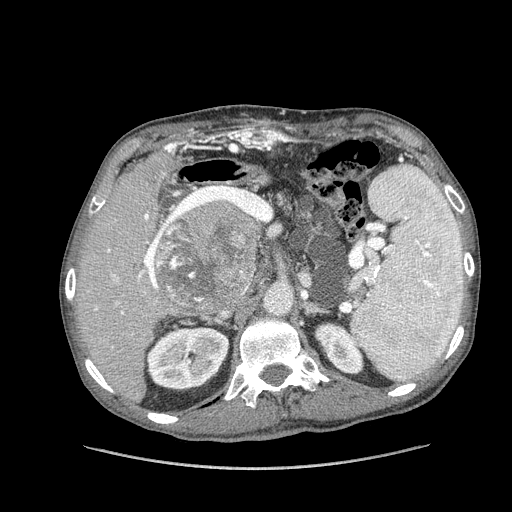
Contrast-enhanced abdominal CT (liver protocol), one axial slice; soft-tissue window (W 400 / L 40 HU); 2.5 mm slice thickness; 512 × 512 image matrix, field of view 400 × 400 mm. From the clinical record (not read from this slice): diagnosis: hepatocellular carcinoma (patient treated with transarterial chemoembolisation; whether this scan precedes or follows treatment is not stated here); TNM stage (as recorded): Stage-IIIA.
Outlined on this slice (semi-automatic segmentation, software-assisted and operator-edited):
- liver parenchyma outside the tumour (the mass and vessels are separate outlines, so this box may not span the whole liver): bounding box [x1, y1, x2, y2] px = [78, 148, 262, 402]
- mass: [154, 200, 259, 310]
- liver vessels: [95, 214, 179, 391]